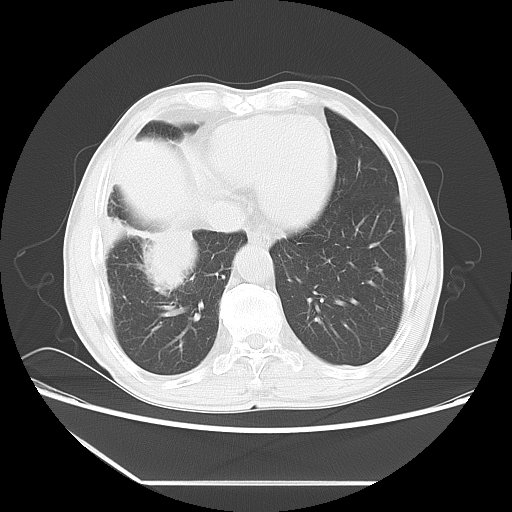
Chest CT, one axial slice; slice 19 of 60 in the series (ordered by position); reconstruction kernel LUNG; 120 kVp; lung window (W 1500 / L -600 HU); 512 × 512 image matrix, field of view 386 × 386 mm. Male patient, age 72 years. From the clinical record (not read from this slice): clinical TNM (as recorded): T1c N0 M0.
Outlined on this slice (rectangle marked by the reading radiologist):
- lung tumour (recorded histology: squamous cell carcinoma): bounding box <116,224,198,309> (left, top, right, bottom; pixels)